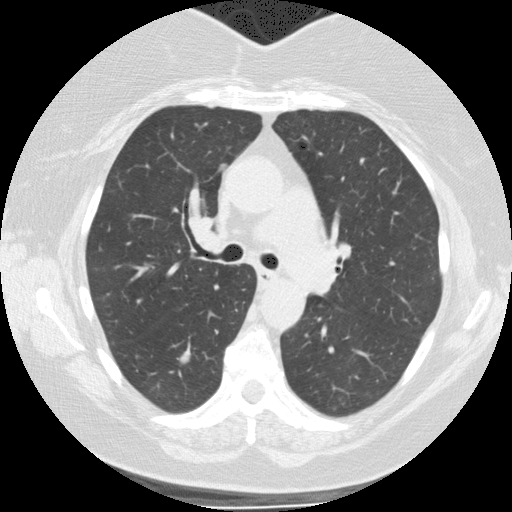
Low-dose screening chest CT, axial slice, baseline annual screen, lung window (W 1500 / L -600 HU), 120 kVp, slice 47 of 130 in the series. Female participant, aged 62 years at enrolment. Current smoker at enrolment.
Lesion marked by an expert reader, bounding box (x1, y1, x2, y2) in pixels: (202, 153, 242, 187). The screening reader recorded 3 non-calcified nodules or masses ≥4 mm on this exam (right lower lobe, right lower lobe, right lower lobe); which of them this box marks is not recorded. Official screen result: positive, change unspecified: nodule(s) >= 4 mm or enlarging nodule(s), mass(es), or other non-specific abnormalities suspicious for lung cancer.